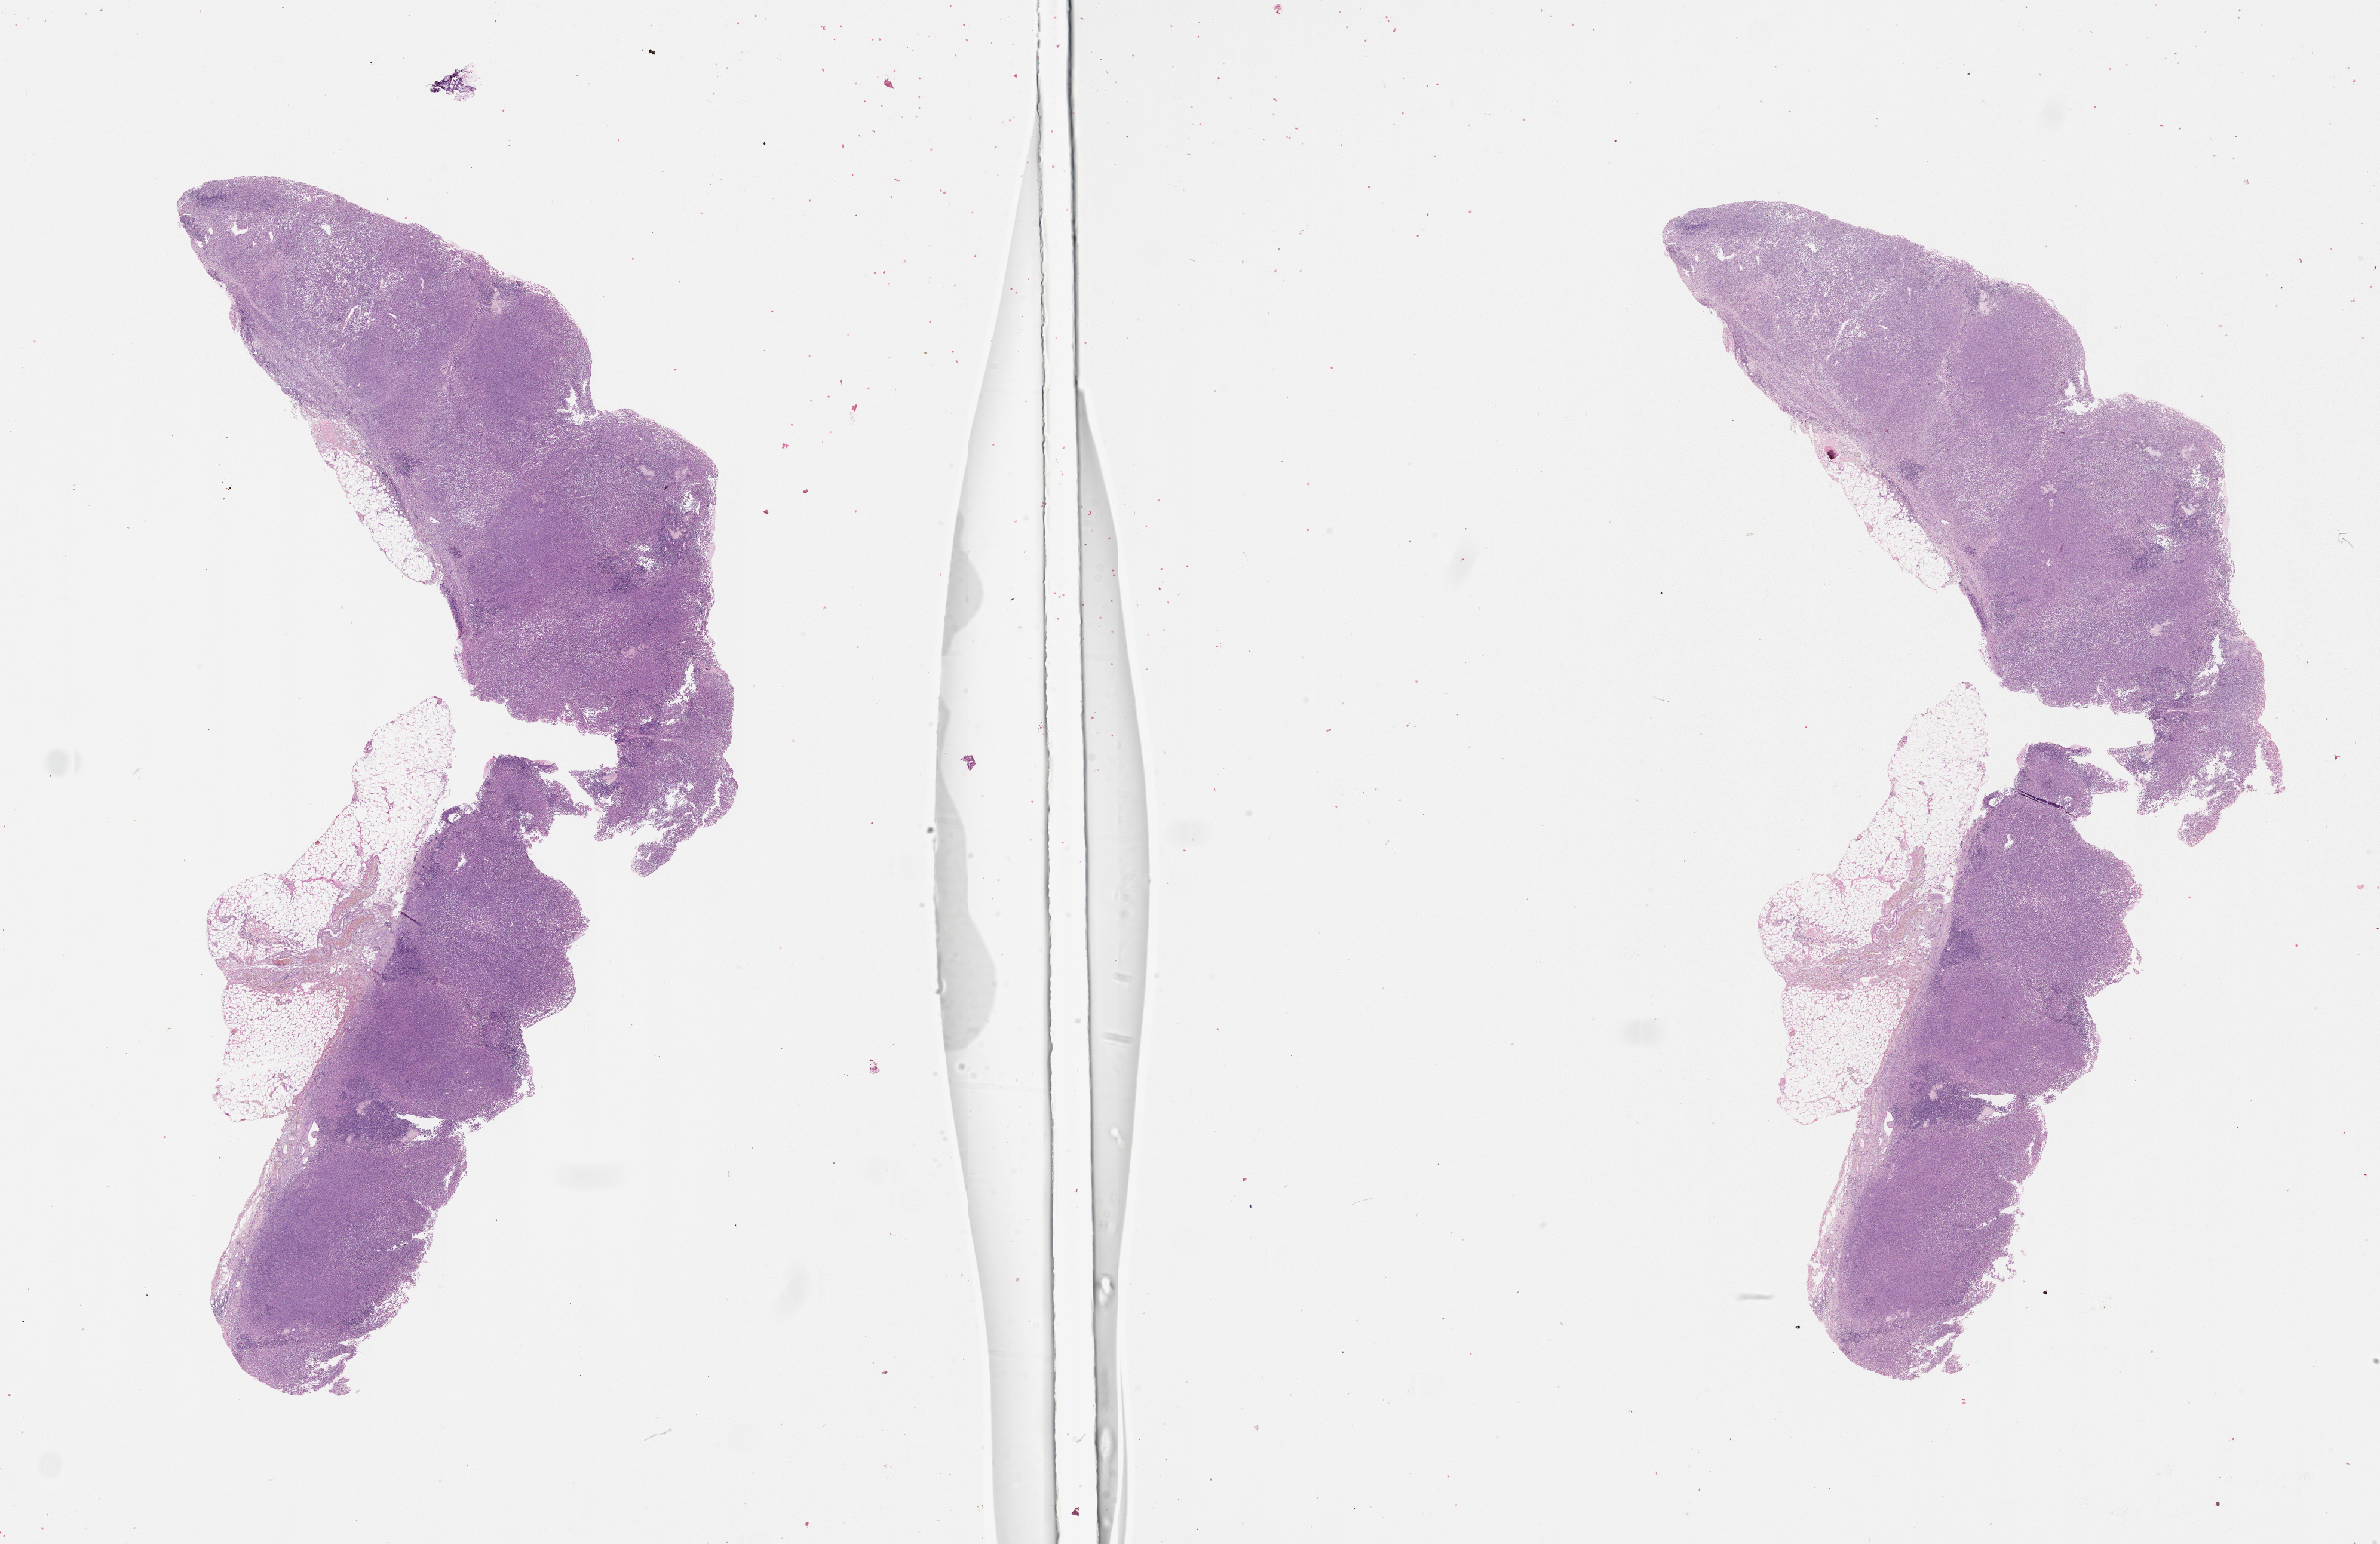
Digitized H&E tissue section (whole slide) — shown as a low-resolution overview of the whole scanned area (about 32.1 x 20.8 mm, from a 20x scan). Female, 80 y/o.
• patient diagnosis: Malignant melanoma, NOS